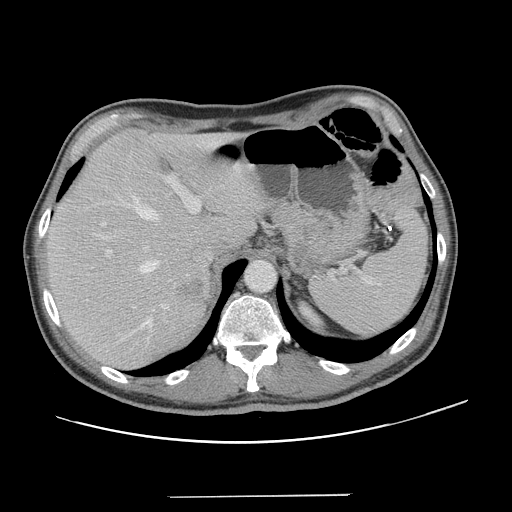
Contrast-enhanced abdominal CT, one axial slice. Position 96 of 131 along the scan axis. 120 kVp. Intravenous contrast given. Soft-tissue window (W 400 / L 40 HU). 2.5 mm slice thickness. 512 × 512 image matrix. Male patient, age 60 years. Case-level facts recorded for this patient, not image findings: diagnosis: colorectal cancer liver metastases, imaged before liver resection; multiple liver metastases: no; largest metastasis: 2.5 cm; disease in both lobes: no.
Structures marked on this image (expert manual segmentation):
- hepatic veins: box from (x=94, y=195) to (x=160, y=328) px
- liver: (x=47, y=131)–(x=257, y=369)
- planned liver remnant (the part of the liver to remain after resection): (x=47, y=131)–(x=256, y=353)
- portal vein (with intrahepatic branches): (x=99, y=144)–(x=205, y=258)
- liver metastasis: (x=174, y=278)–(x=207, y=302)